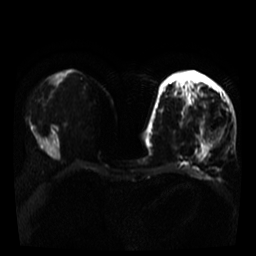
Breast MRI, one axial slice. Diffusion-weighted series; image 2 of 4 stored at this slice position (different b-values; order by instance number). 3 T. 256 × 256 image matrix, field of view 320 × 320 mm. Female patient.
Annotated regions visible in this slice (expert manual segmentation):
- tumour on diffusion-weighted imaging: bounding box (x1, y1, x2, y2) in pixels: (213, 129, 223, 141)